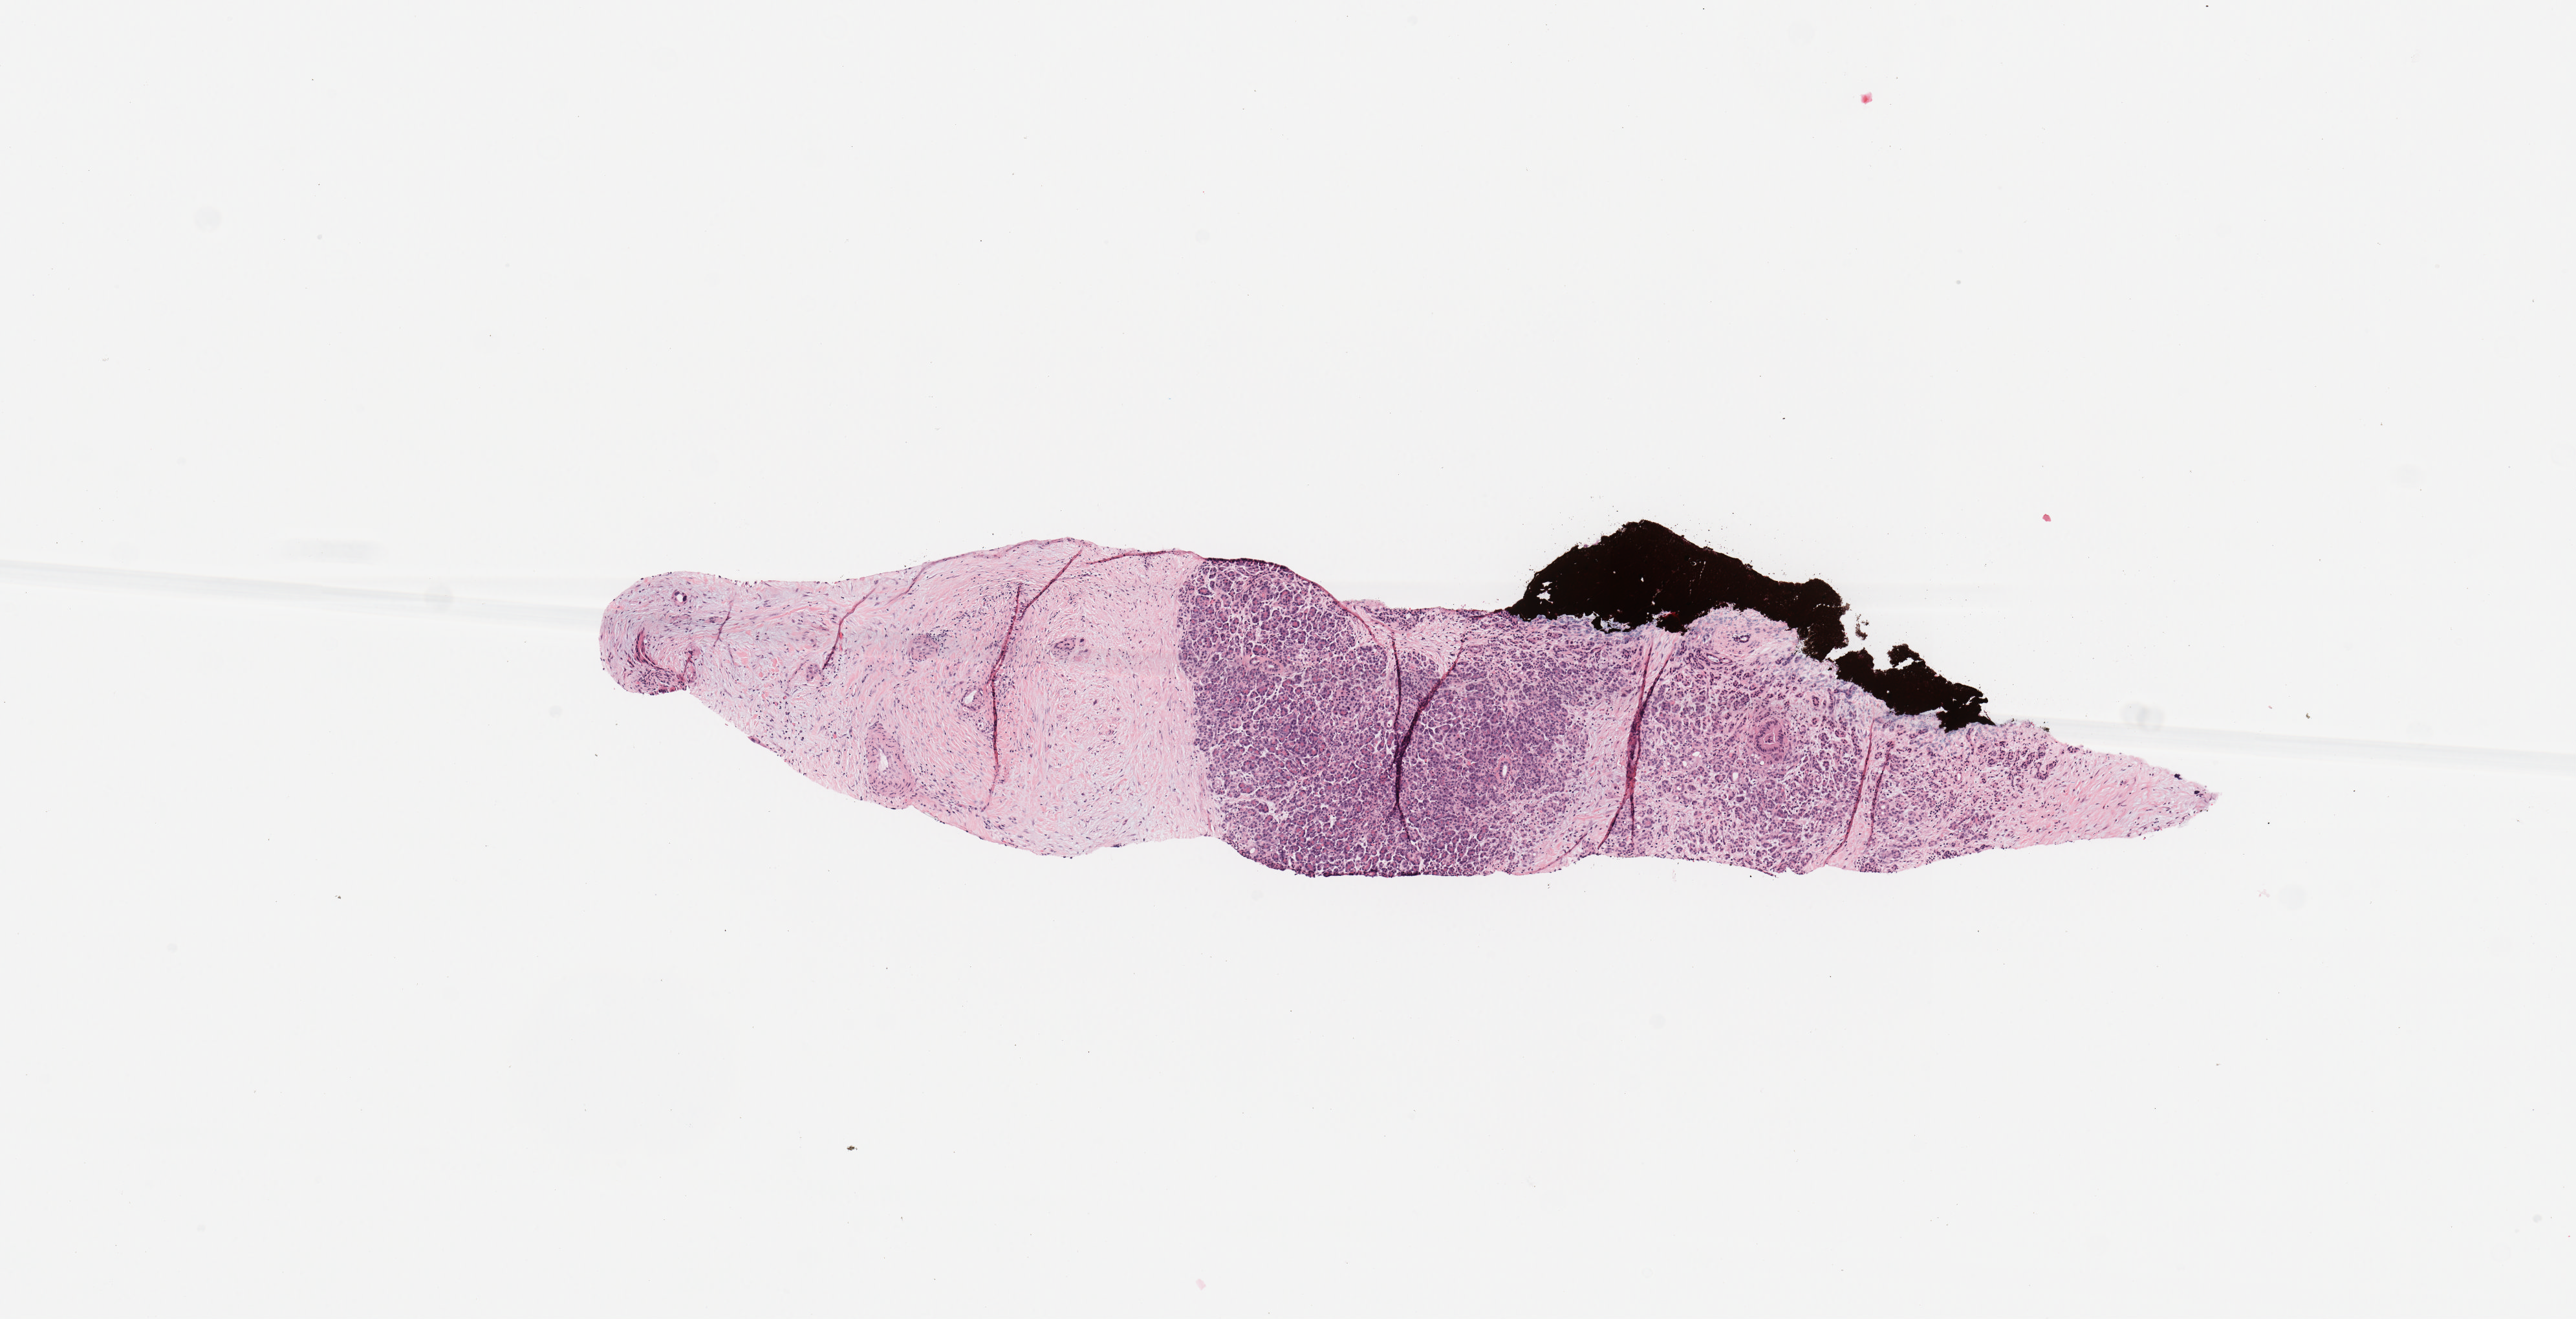
Digitized Hematoxylin and eosin (H&E) stained tissue section (whole slide) — shown as a low-resolution overview of the whole scanned area (about 7.9 x 4.0 mm, acquisition: 20x scan); tumour tissue sample, pancreas. Female, 36 y/o. Histologic grade: G2 (moderately differentiated).
AJCC pathologic stage: III. Histologic diagnosis: Infiltrating duct carcinoma, NOS.